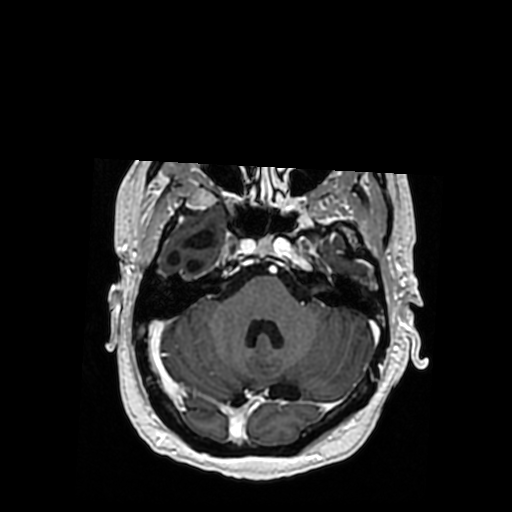
Brain MRI from a brain-tumour surgery series, one axial slice; slice 254 of 364 in the series (ordered by position); T1-weighted post-contrast; 0.5 mm slice thickness; 512 × 512 image matrix. From the clinical record (not read from this slice): histopathology: Oligodendroglioma; WHO grade: 3; IDH mutation: yes.
Annotated regions visible in this slice (manually delineated by an expert):
- previous resection cavity: bounding box (x1, y1, x2, y2) in pixels: (168, 229, 214, 273)